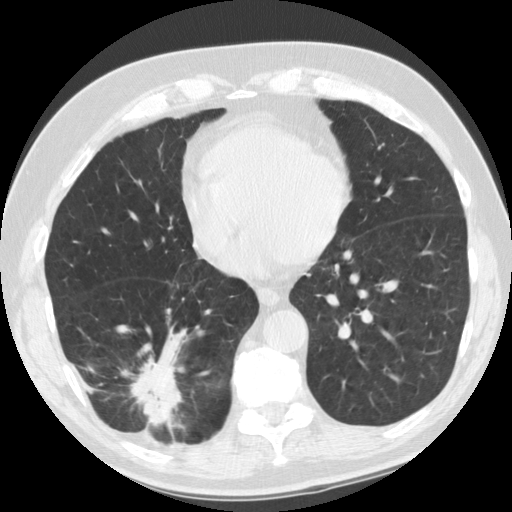
Axial slice from a low-dose chest CT screening exam, baseline screening round, lung window (W 1500 / L -600 HU), 2.5 mm slice thickness, 512 × 512 image matrix, field of view 340 × 340 mm. Male, age 69 years at enrolment. Former smoker at enrolment.
- Lesion marked by an expert reader, bounding box <105,331,191,440> (left, top, right, bottom; pixels).
- The screening reader recorded 2 non-calcified nodules or masses ≥4 mm on this exam; which of them this box marks is not recorded.
- Later outcome: lung cancer diagnosed 40 days after this screen — adenocarcinoma, NOS, right lower lobe, stage IIB (AJCC 6th edition), 45 mm at pathology.